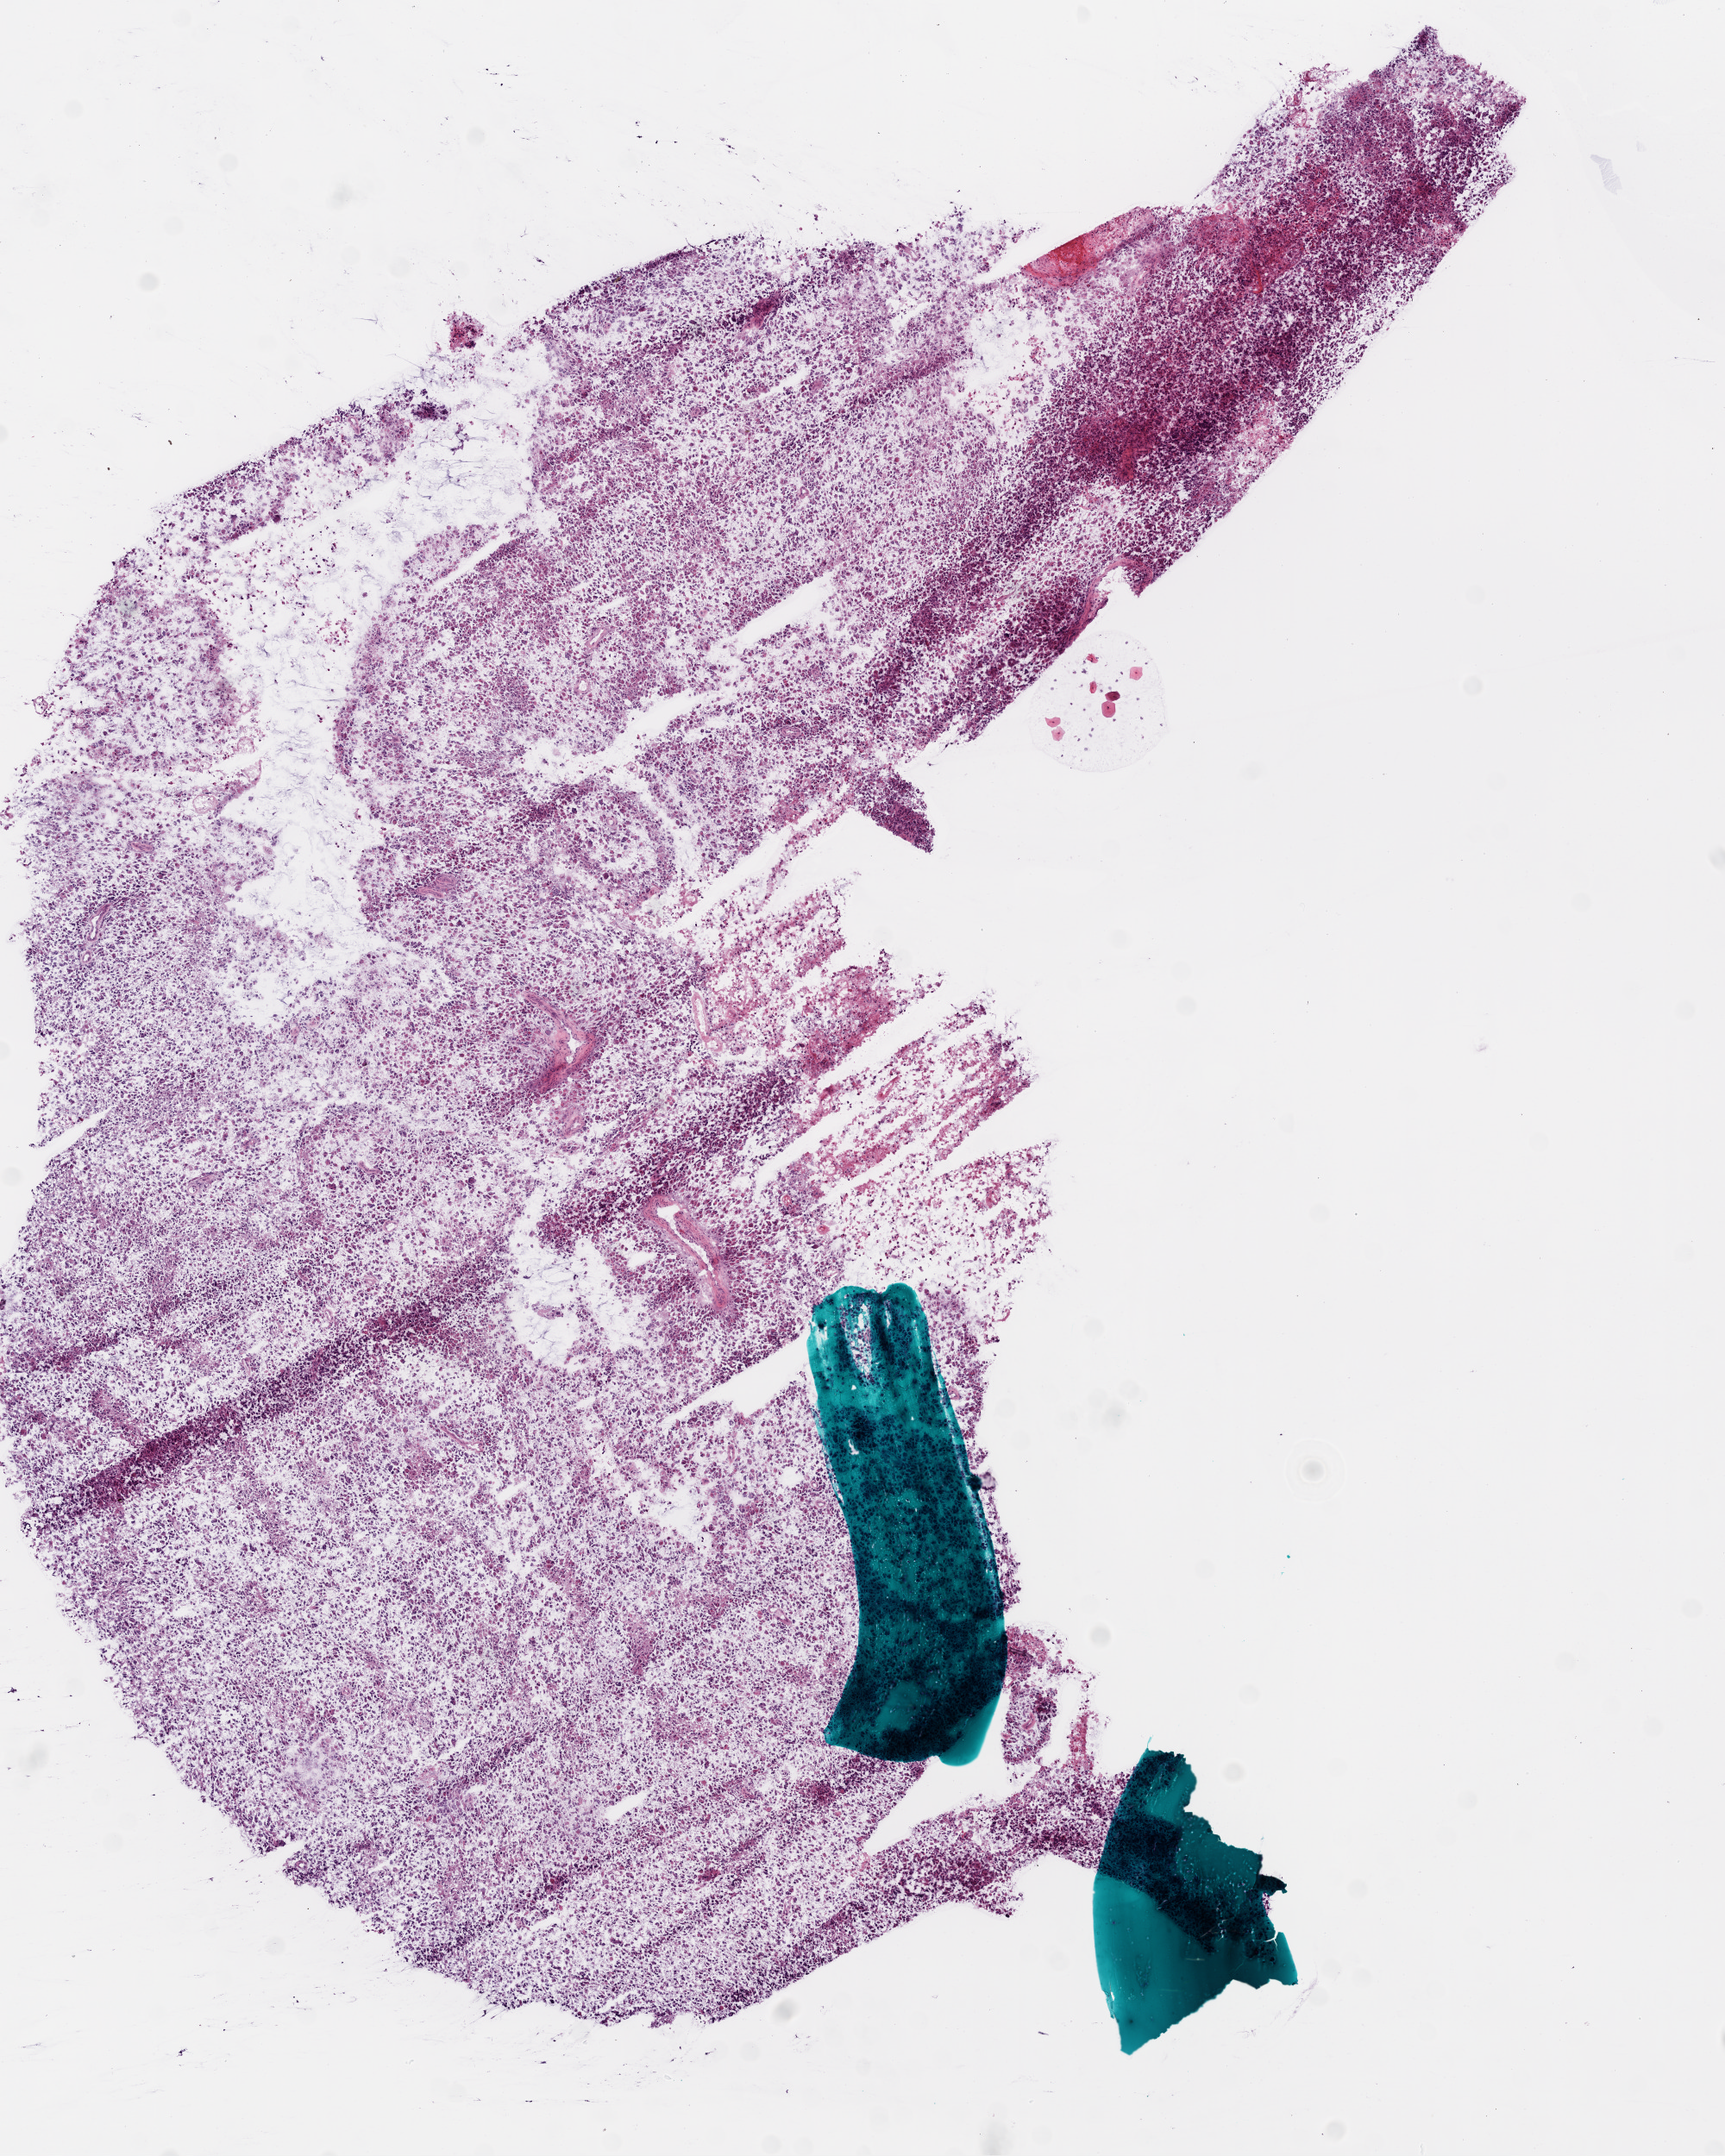
Digitized H&E tissue section (whole slide), a low-resolution overview of the entire scanned area, about 8.0 x 10.0 mm (acquisition: 20x scan). Frozen section. Brain, primary tumour sample. Female patient; age at initial diagnosis 72 years. Composition of this section per pathologist review: tumour cells 80%, tumour nuclei 98%, normal cells 0%, stromal cells 0%, necrosis 20%. Infiltration values recorded for this section: lymphocyte infiltration 100%.
Diagnosis: Glioblastoma.